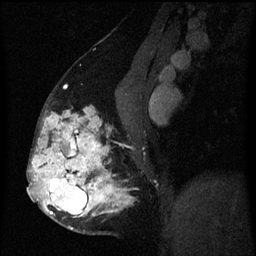
Breast MRI (dynamic contrast-enhanced), one sagittal slice; position 31 of 60 along the scan axis; dynamic contrast-enhanced series, image 2 of 3 at this slice position (ordered by acquisition); 1.5 T; TE 4.2 ms, TR 8 ms; 2 mm slice thickness; 256 × 256 image matrix. Female patient, age 50 years.
Structures marked on this image (semi-automatically segmented with operator editing):
- analysis volume of interest (the breast-tissue region the enhancement analysis was run in; not a lesion): bounding box <32,102,130,233> (left, top, right, bottom; pixels)
- tumour enhancement mask (voxels above the 70 % enhancement threshold inside the analysis volume of interest): <32,108,129,230>